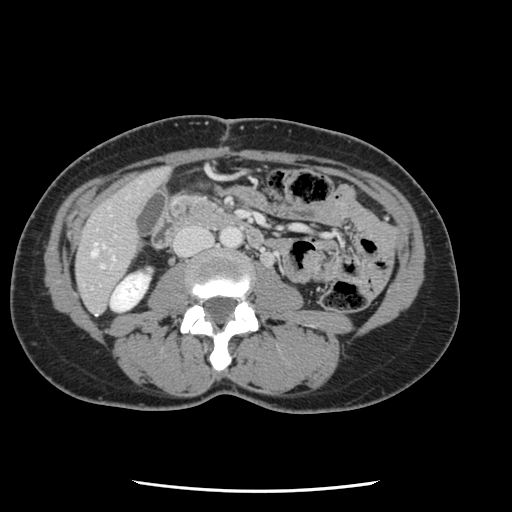
Contrast-enhanced abdominal CT, one axial slice. Slice 22 of 134 in the series (ordered by position). 120 kVp. Intravenous contrast given. Soft-tissue window (W 400 / L 40 HU). 2.5 mm slice thickness. 512 × 512 image matrix. Female patient, age 43 years. From the clinical record (not read from this slice): diagnosis: colorectal cancer liver metastases, imaged before liver resection; multiple liver metastases: yes; largest metastasis: 3.4 cm.
Structures marked on this image (manually delineated by an expert):
- hepatic veins: bounding box <92,244,97,256> (left, top, right, bottom; pixels)
- liver: <77,169,169,313>
- planned liver remnant (the part of the liver to remain after resection): <77,169,169,313>